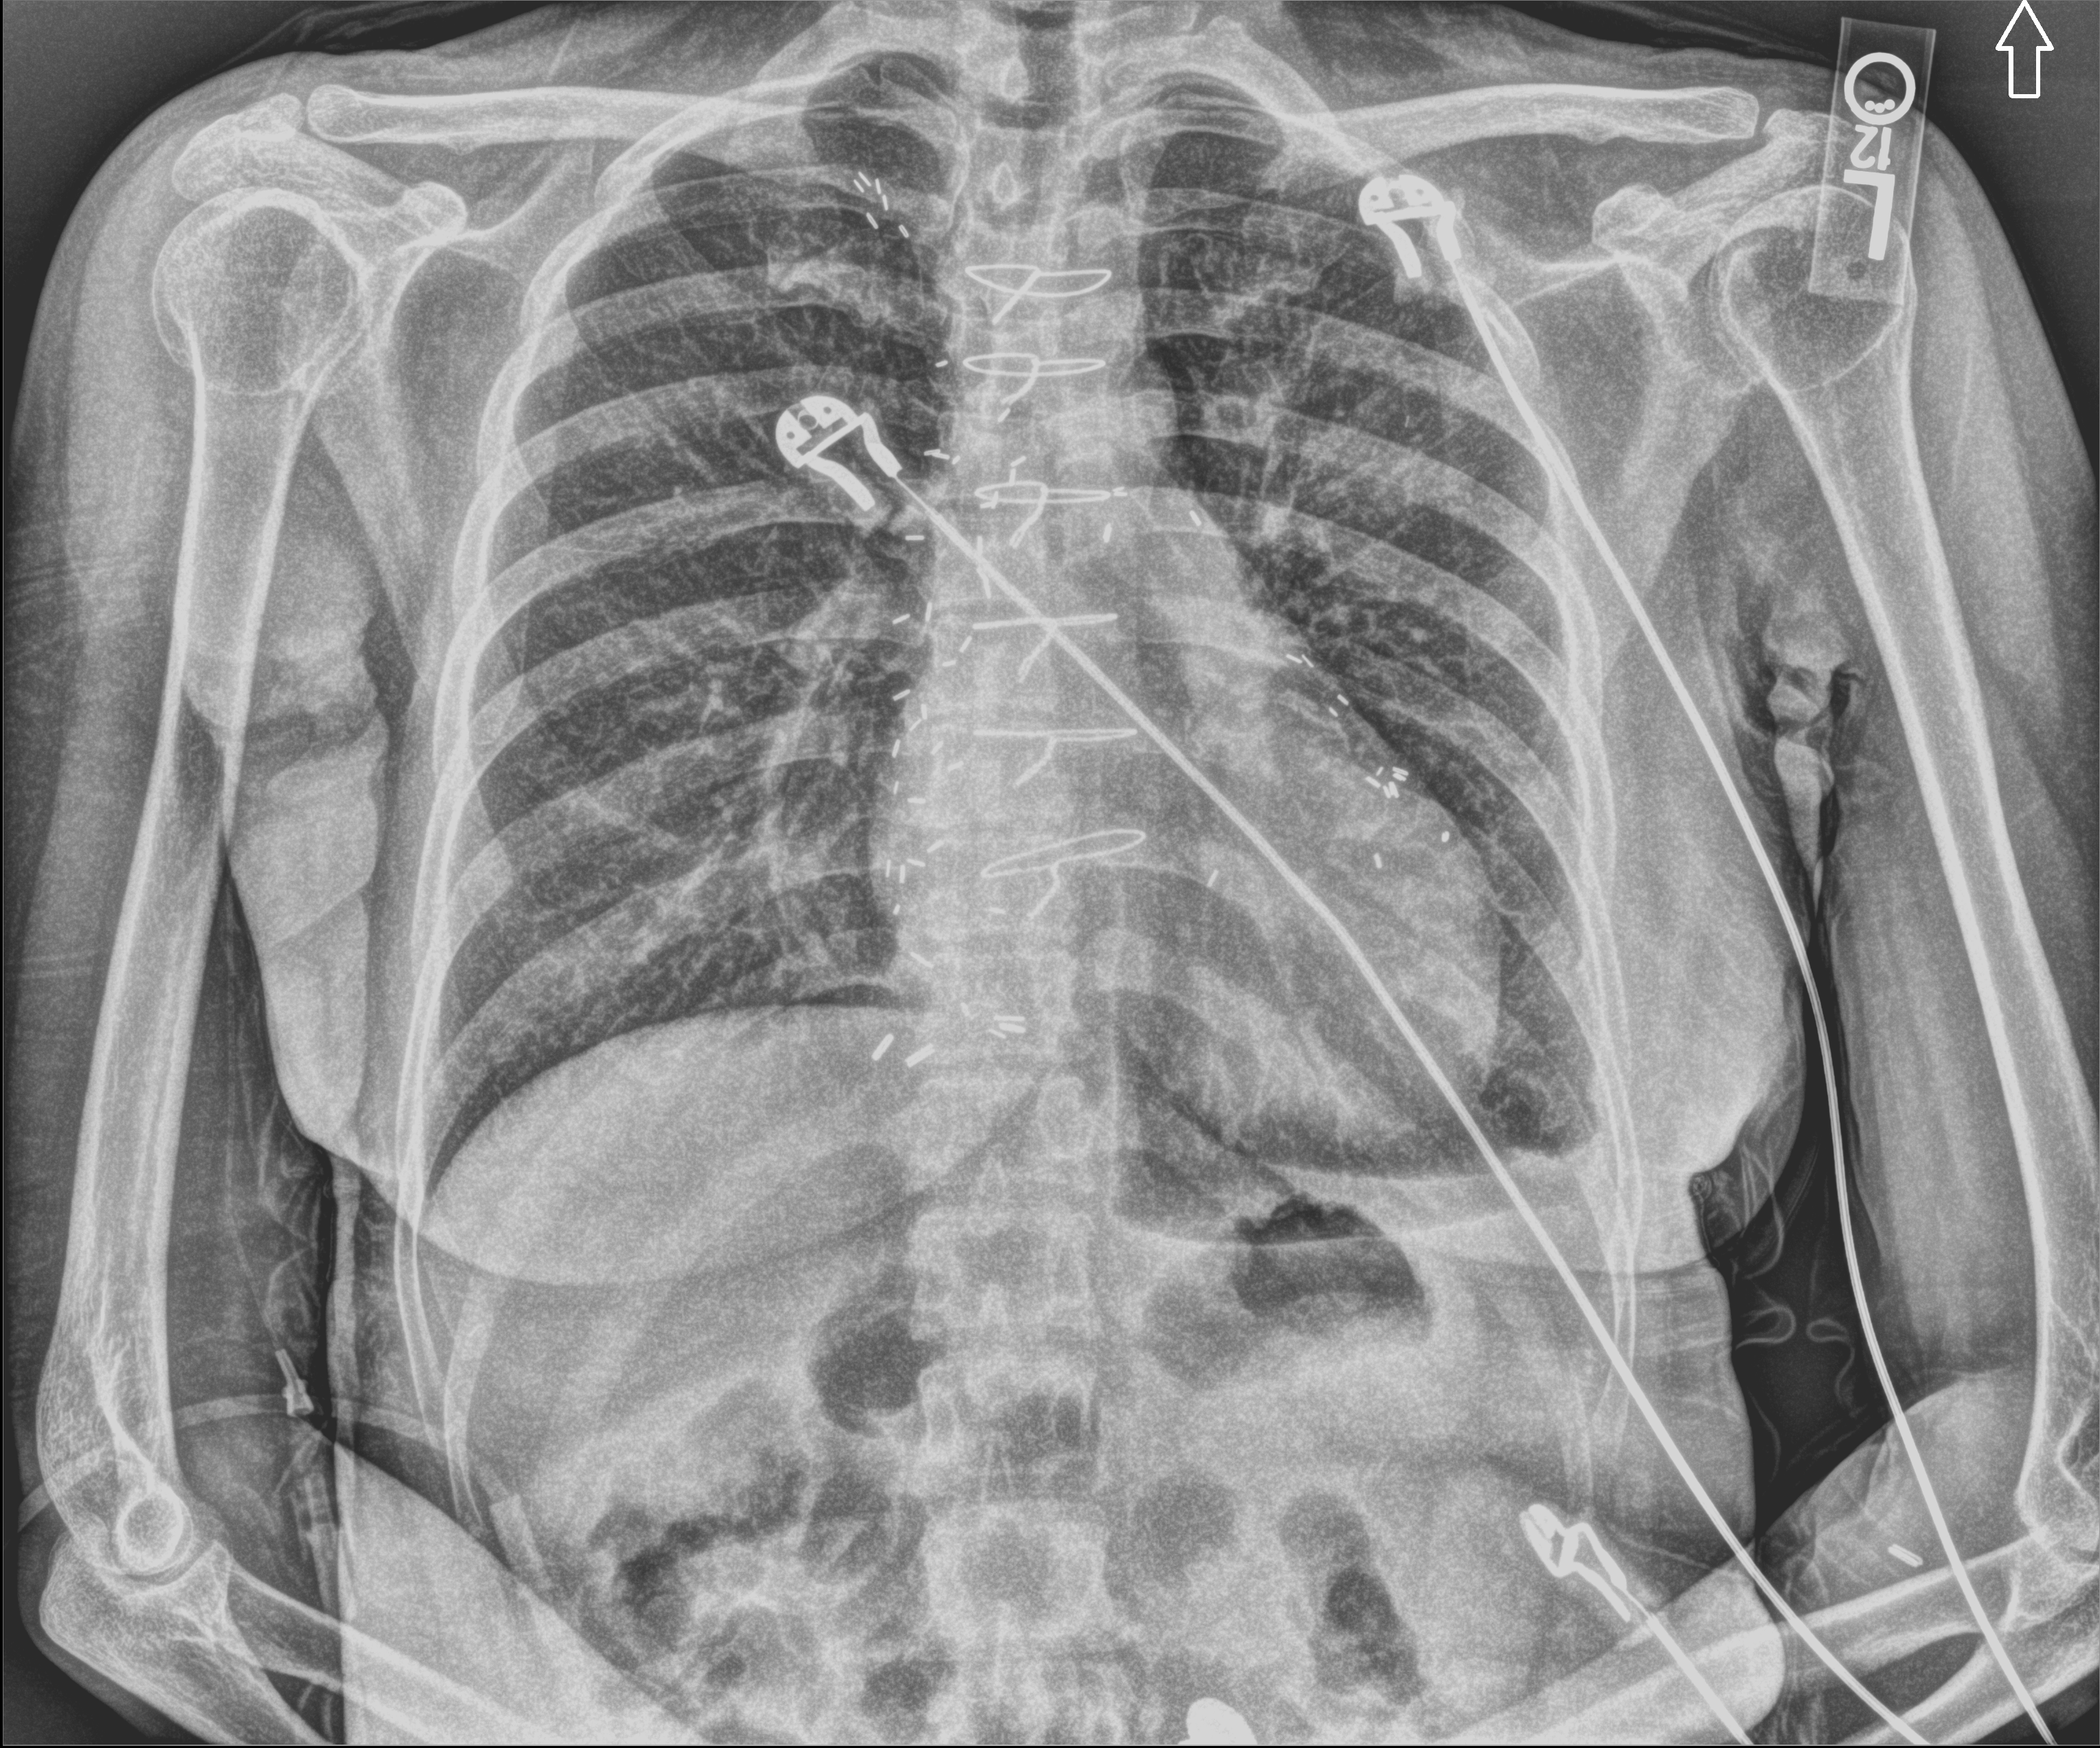
Bedside chest radiograph (computed radiography). Patient hospitalised with COVID-19; male, aged 18–59 years.
Admission-level facts for this patient (not findings on this image; timing relative to this image not recorded):
- mechanically ventilated during this hospital stay: no
- smoking status (admission record): never
- admitted to intensive care during this hospital stay: no